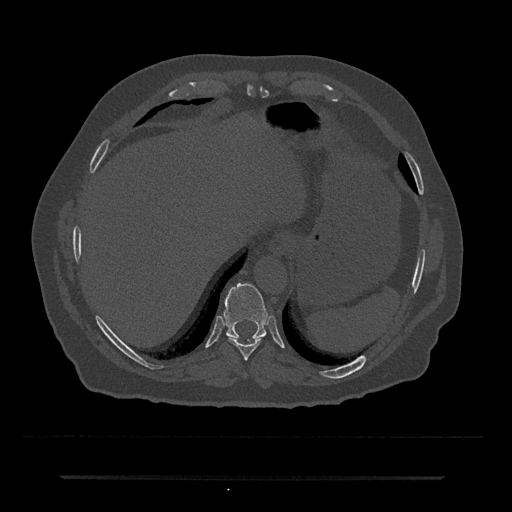
CT including the spine, one axial slice; position 254 of 797 along the scan axis; reconstruction kernel Br40s/3; 120 kVp; bone window (W 1800 / L 400 HU); 0.5 mm slice thickness; 512 × 512 image matrix, field of view 437 × 437 mm. Male patient, age 69 years. Case-level facts recorded for this patient, not image findings: primary cancer: prostate.
Annotated regions visible in this slice (semi-automatically segmented with operator editing):
- T10 vertebra: bounding box [x1, y1, x2, y2] px = [224, 283, 268, 340]
- T9 vertebra: [227, 336, 261, 360]